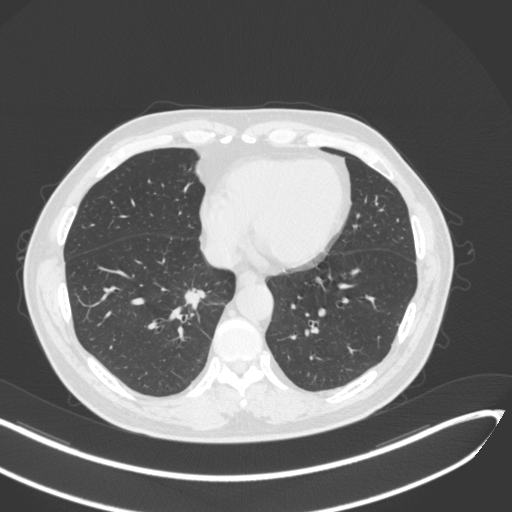
Chest CT, one axial slice. Position 128 of 429 along the scan axis. 120 kVp. Lung window (W 1500 / L -600 HU). 1 mm slice thickness. 512 × 512 image matrix. Male patient, age 62 years. From the clinical record (not read from this slice): clinical TNM (as recorded): T1b N0 M0.
Outlined on this slice (bounding box drawn by a radiologist):
- lung tumour (recorded histology: adenocarcinoma): bounding box (x1, y1, x2, y2) in pixels: (181, 286, 215, 313)